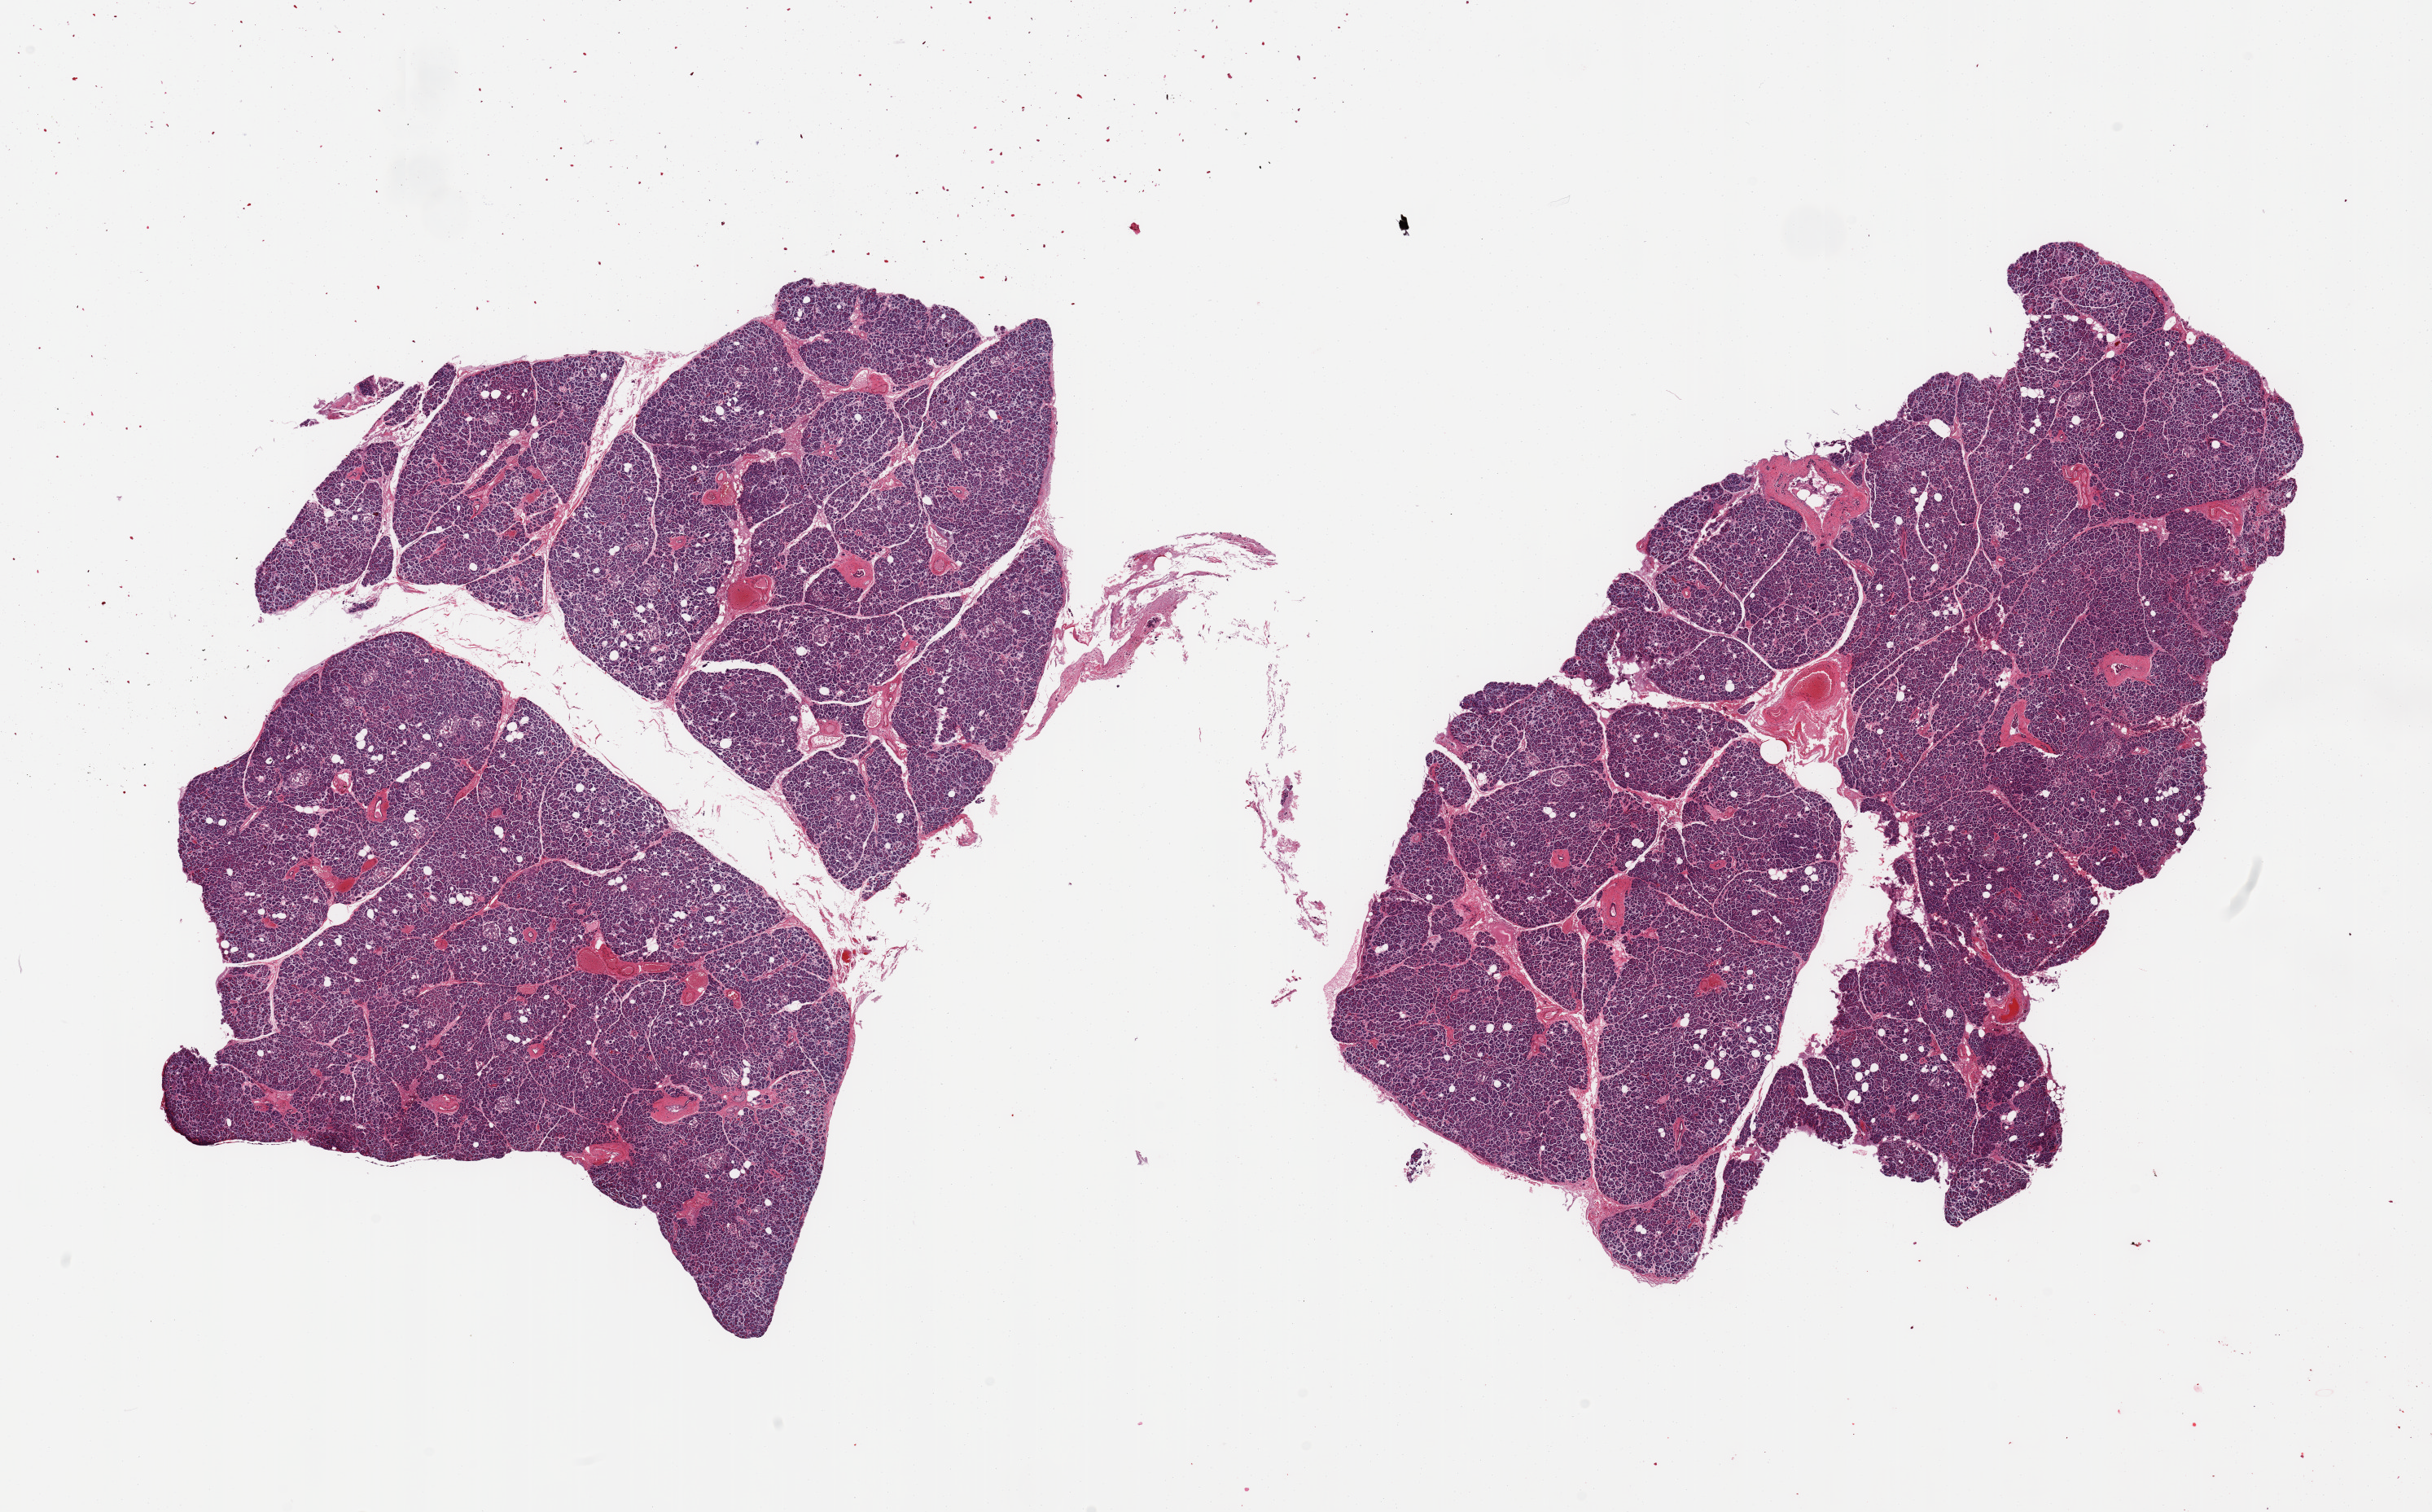
Digitized hematoxylin and eosin (H&E)-stained section — low-resolution overview of the scanned area, about 23.6 x 14.7 mm (acquisition: 20x scan), PAXgene-fixed paraffin-embedded (PFPE) section, section of pancreas (target tissue), donor tissue sample. Female donor.
• review note (as recorded): 2 pieces, mildl-moderate saponification; islets still visible, but with early degenerative changes